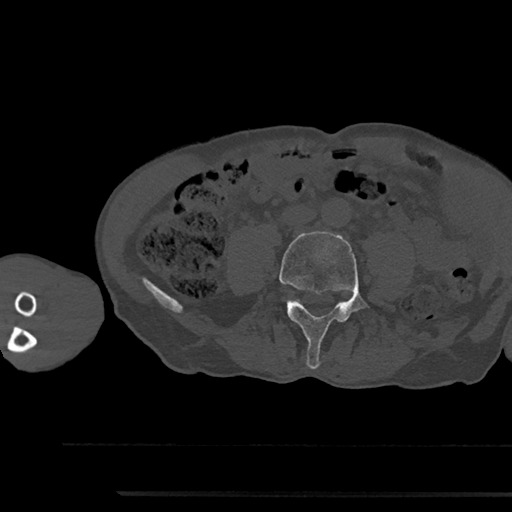
CT including the spine, one axial slice. Position 407 of 797 along the scan axis. Reconstruction kernel Br40s/3. Bone window (W 1800 / L 400 HU). 0.5 mm slice thickness. 512 × 512 image matrix. Patient: male, 79 years. From the clinical record (not read from this slice): primary cancer: prostate.
Annotated regions visible in this slice (semi-automatic segmentation, software-assisted and operator-edited):
- L4 vertebra: bounding box <279,231,365,369> (left, top, right, bottom; pixels)